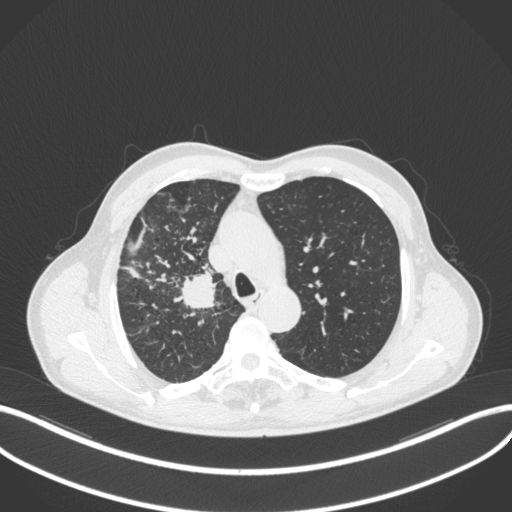
Chest CT, one axial slice; position 349 of 490 along the scan axis; reconstruction kernel B31f; 120 kVp; lung window (W 1500 / L -600 HU); 512 × 512 image matrix, field of view 400 × 400 mm. Male patient, age 69 years. From the clinical record (not read from this slice): clinical TNM (as recorded): T2a N0 M0.
Structures marked on this image (bounding box drawn by a radiologist):
- lung tumour (recorded histology: adenocarcinoma): bounding box [x1, y1, x2, y2] px = [176, 265, 224, 313]